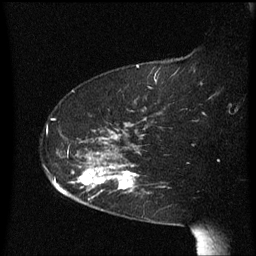
Breast MRI (dynamic contrast-enhanced), one sagittal slice. Slice 45 of 60 in the series (ordered by position). Dynamic contrast-enhanced series, image 2 of 3 at this slice position (ordered by acquisition). 1.5 T. TE 4.2 ms, TR 8.4 ms. 2.3 mm slice thickness. 256 × 256 image matrix, field of view 200 × 200 mm. Female patient, age 63 years. Case-level facts recorded for this patient, not image findings: setting: breast cancer imaged before/during neoadjuvant chemotherapy; receptor status: HER2-positive.
Structures marked on this image (semi-automatic segmentation, software-assisted and operator-edited):
- analysis volume of interest (the breast-tissue region the enhancement analysis was run in; not a lesion): bounding box <71,144,142,207> (left, top, right, bottom; pixels)
- tumour enhancement mask (voxels above the 70 % enhancement threshold inside the analysis volume of interest): <79,164,140,191>